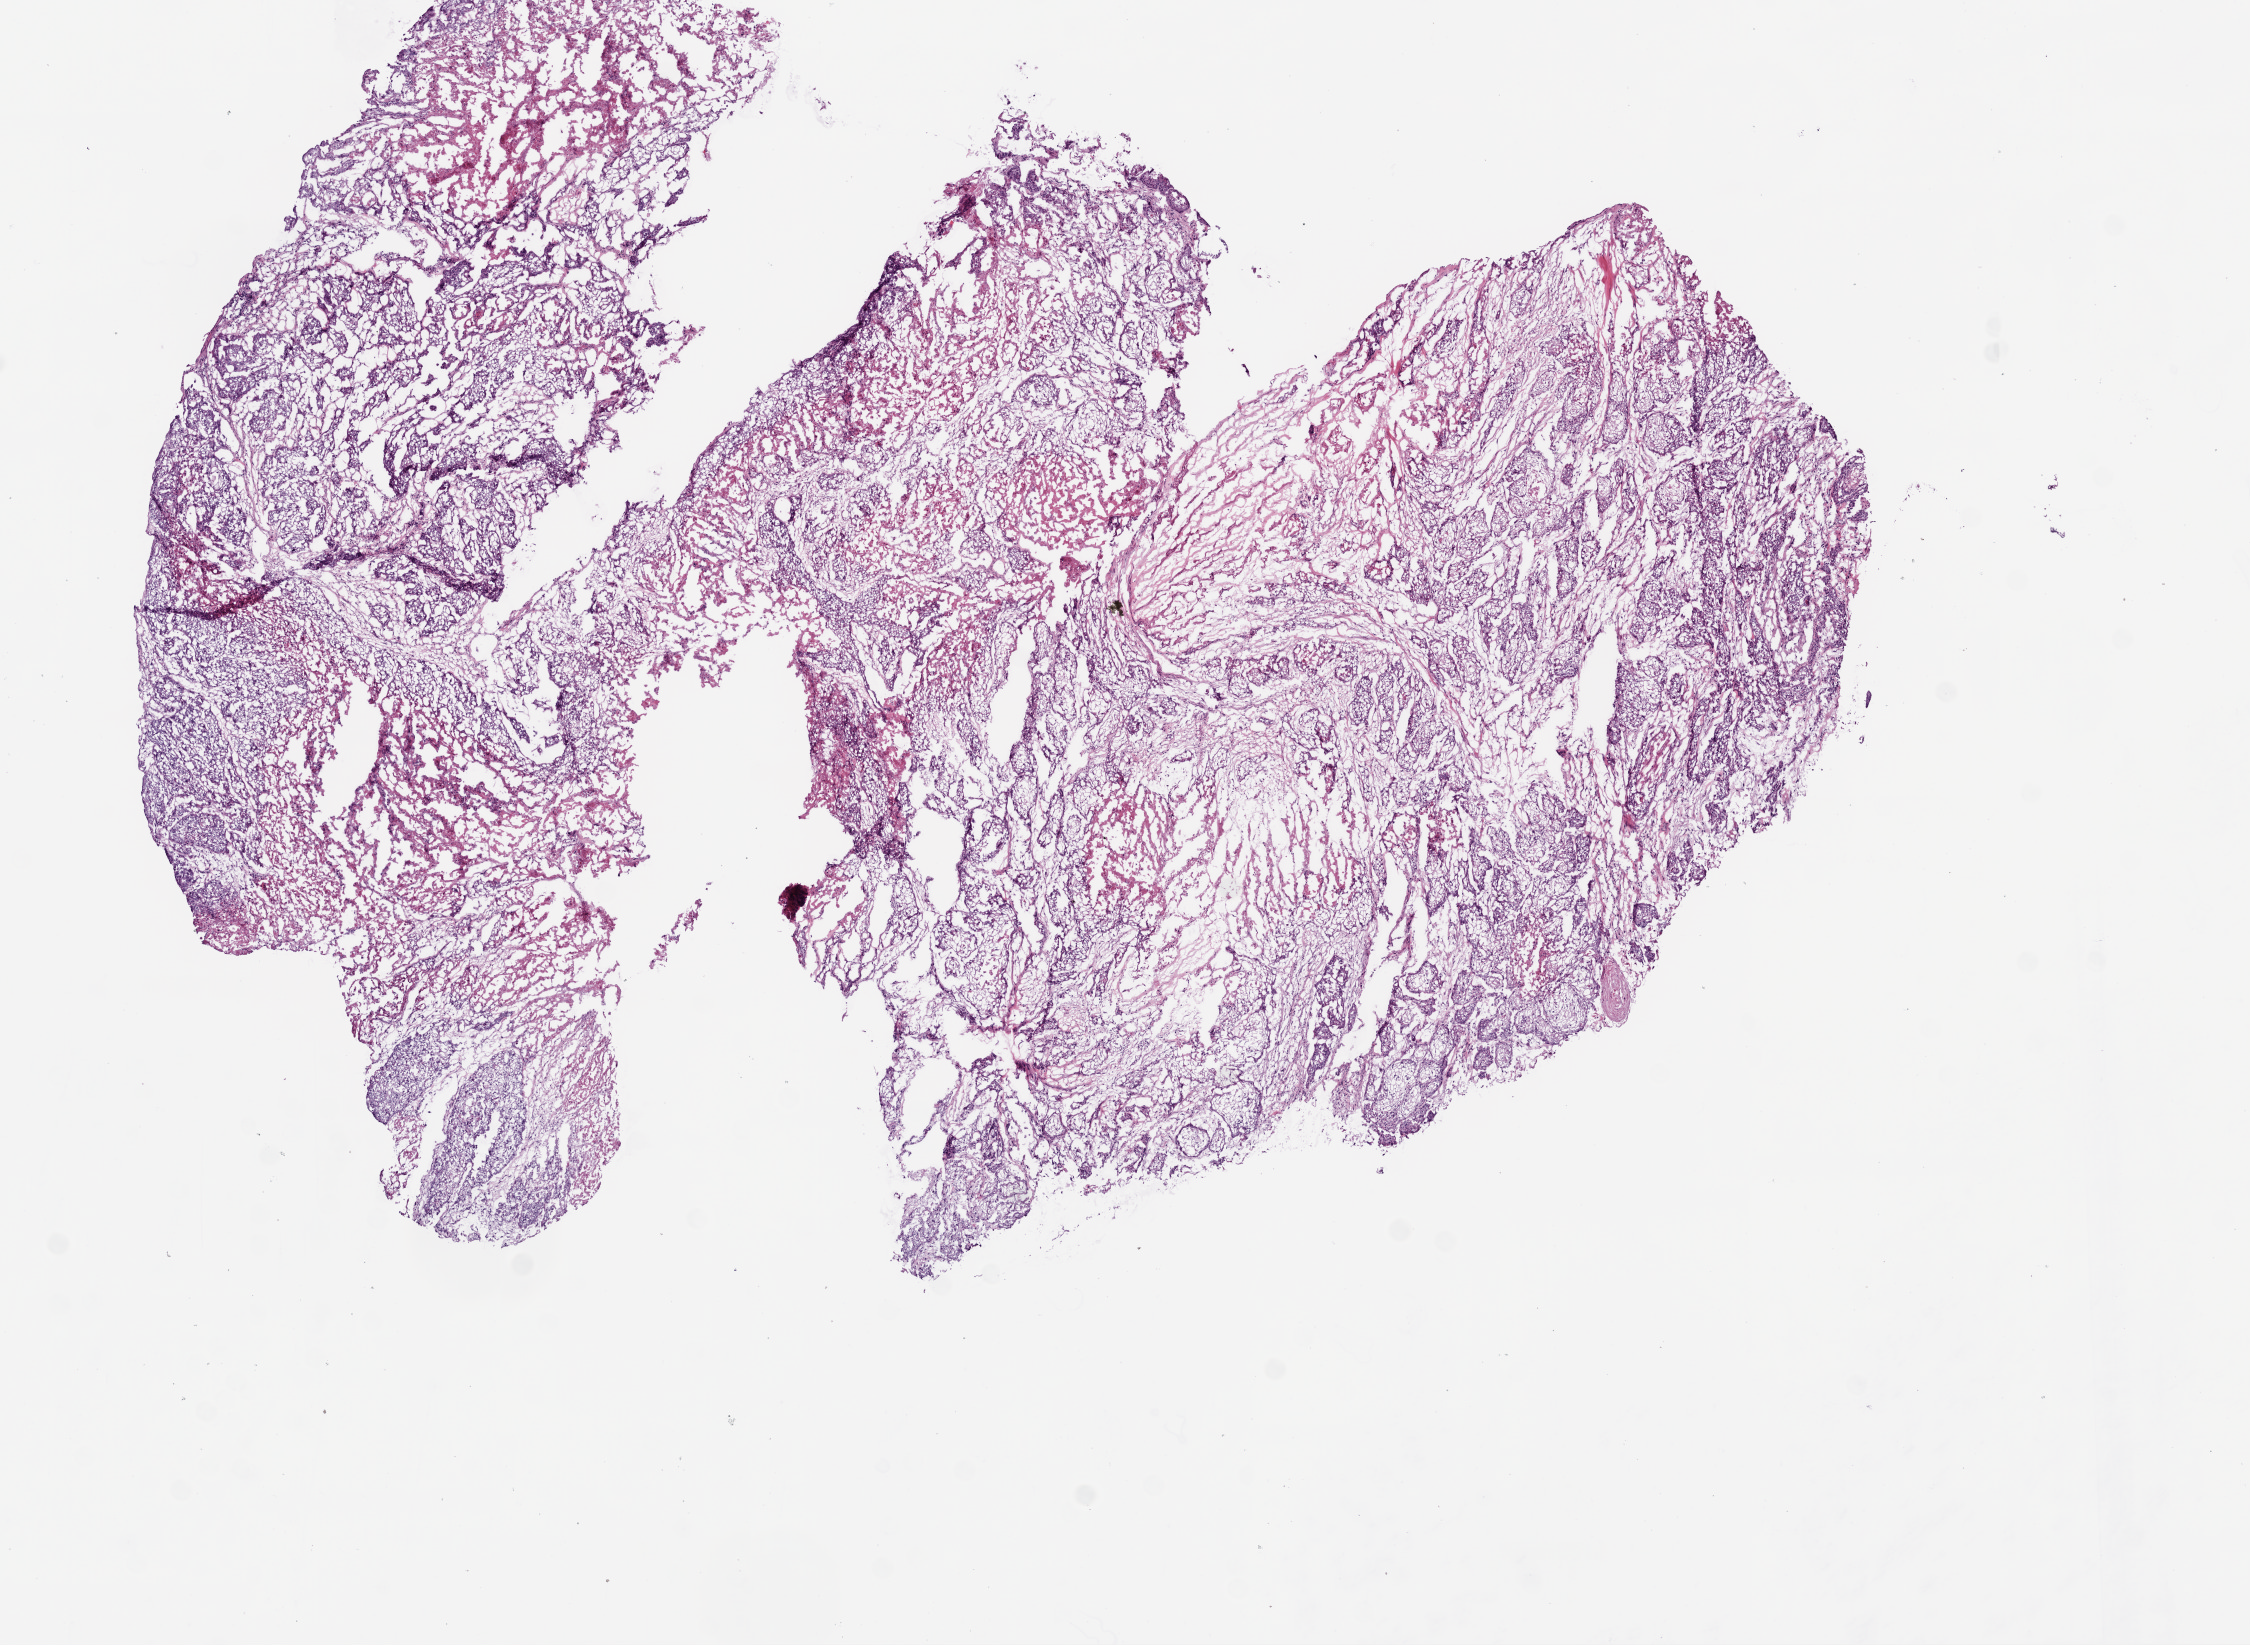
Digitized H&E tissue section (whole slide), low-resolution overview of the scanned area, about 9.0 x 6.6 mm. Frozen section from the bottom of the tissue portion. Head and neck, primary tumour sample. Female, age 63 years at initial diagnosis. Histologic grade: G3 (poorly differentiated). Slide review estimates, as recorded: tumour cells 65%, tumour nuclei 80%, normal cells 0%, stromal cells 30%, necrosis 5%.
TNM: T4a N2c. Diagnosis: Squamous cell carcinoma, NOS (overlapping lesion of lip, oral cavity and pharynx). Lymph nodes positive (case pathology): 3 of 52 examined. AJCC pathologic stage: IVA (7th edition).